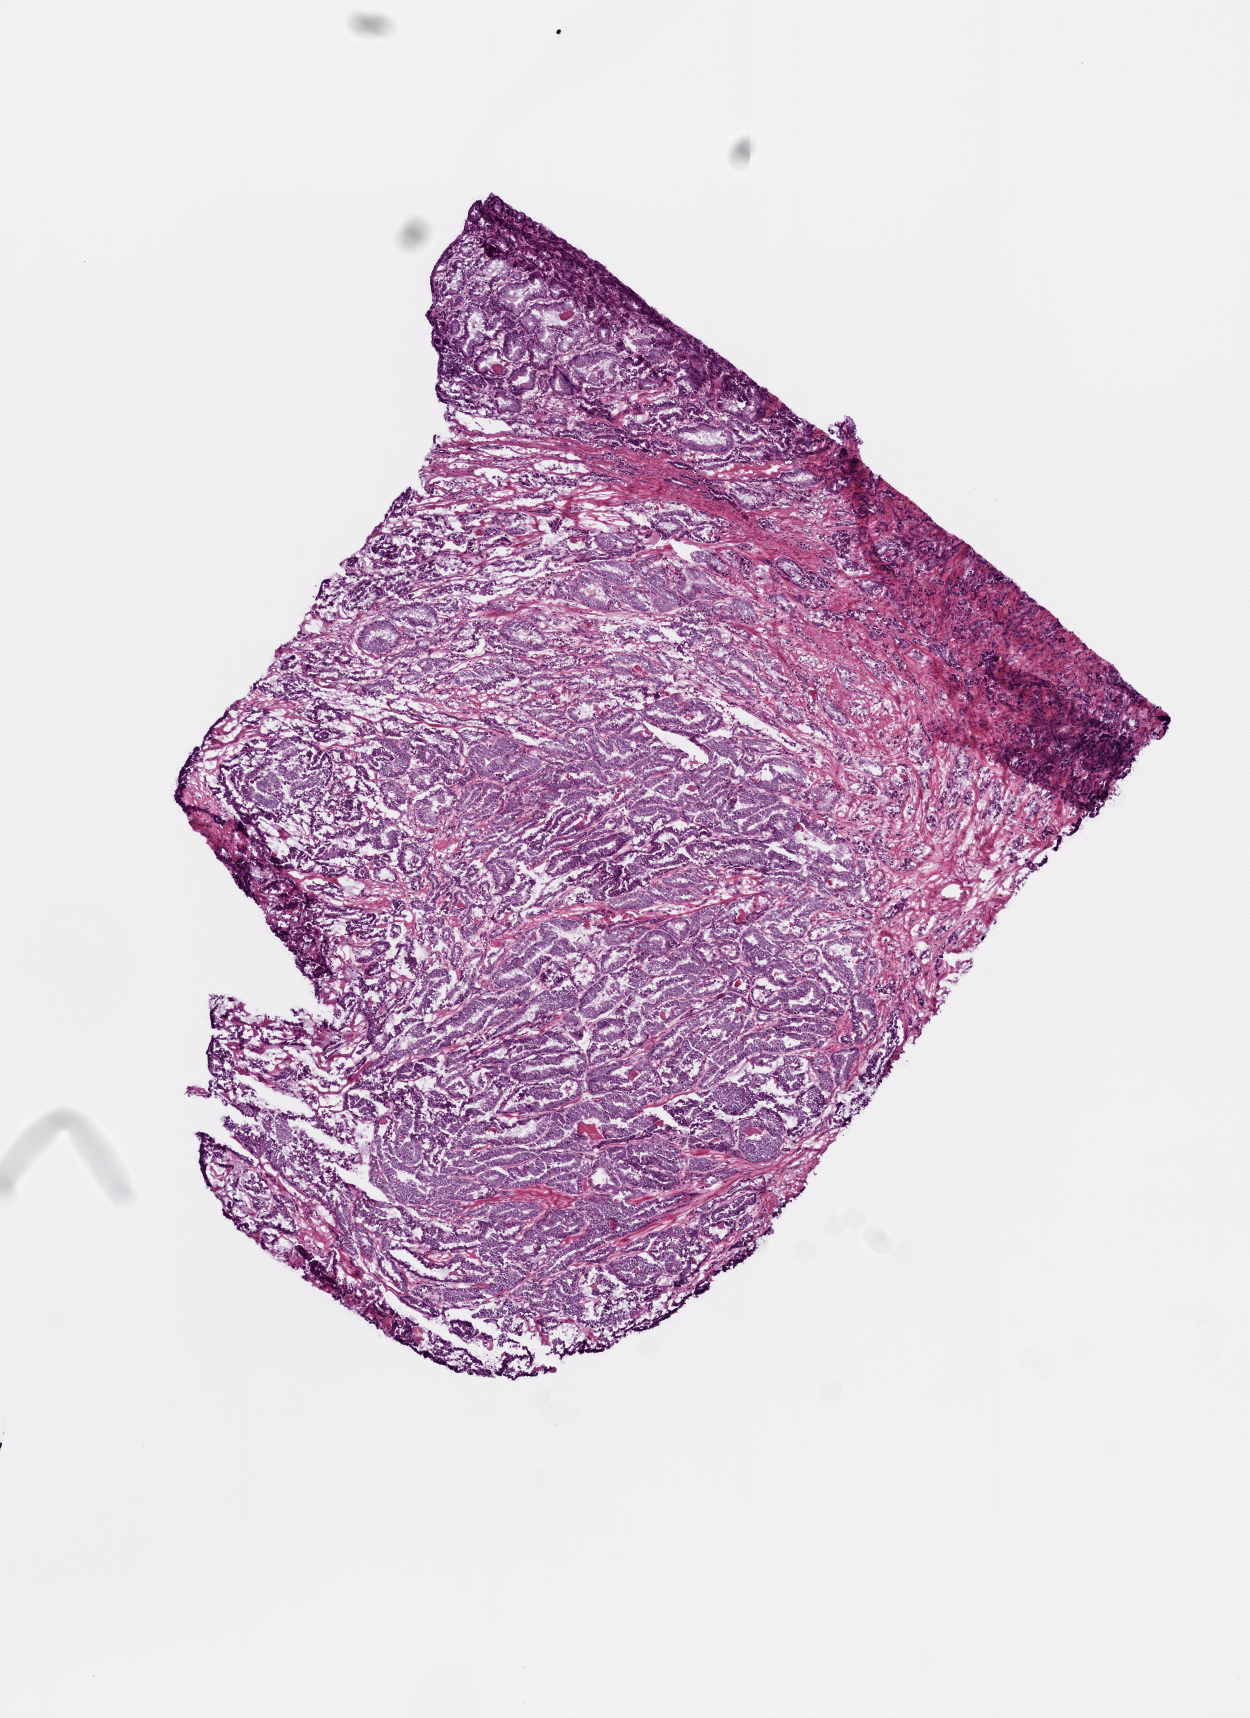
Whole-slide histology image, H&E-stained — whole scanned area (about 5.0 x 6.9 mm, from a 20x scan) shown as a low-resolution overview. Frozen section. Prostate, primary tumour sample. Male, age 73 years at initial diagnosis. Gleason score: 7 (4+3). Pathologist review of this section (percent, as recorded): tumour cells 92%, tumour nuclei 95%, normal cells 1%, stromal cells 7%, necrosis 0%. Infiltration values recorded for this section: lymphocyte infiltration 0%, monocyte infiltration 0%, neutrophil infiltration 0%.
Laterality: bilateral. Pathologic diagnosis: Acinar cell carcinoma (prostate gland).